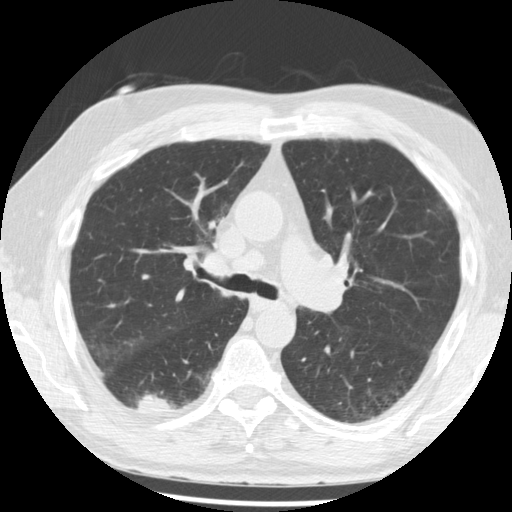
Chest CT (low-dose screening protocol), one axial image; third screening round (two years after baseline); lung window (W 1500 / L -600 HU); standard (soft-tissue) reconstruction kernel (STANDARD); 512 × 512 image matrix. Male, age 68 years at enrolment.
Expert reader's lesion annotation, bounding box (x1, y1, x2, y2) in pixels: (123, 378, 185, 425). The screening reader recorded 3 non-calcified nodules or masses ≥4 mm on this exam (right lower lobe, right lower lobe, right lower lobe); which of them this box marks is not recorded. Later outcome: lung cancer diagnosed 48 days after this screen — squamous cell carcinoma, NOS, right lower lobe, moderately differentiated (G2), stage IB (AJCC 6th edition), 20 mm at pathology.